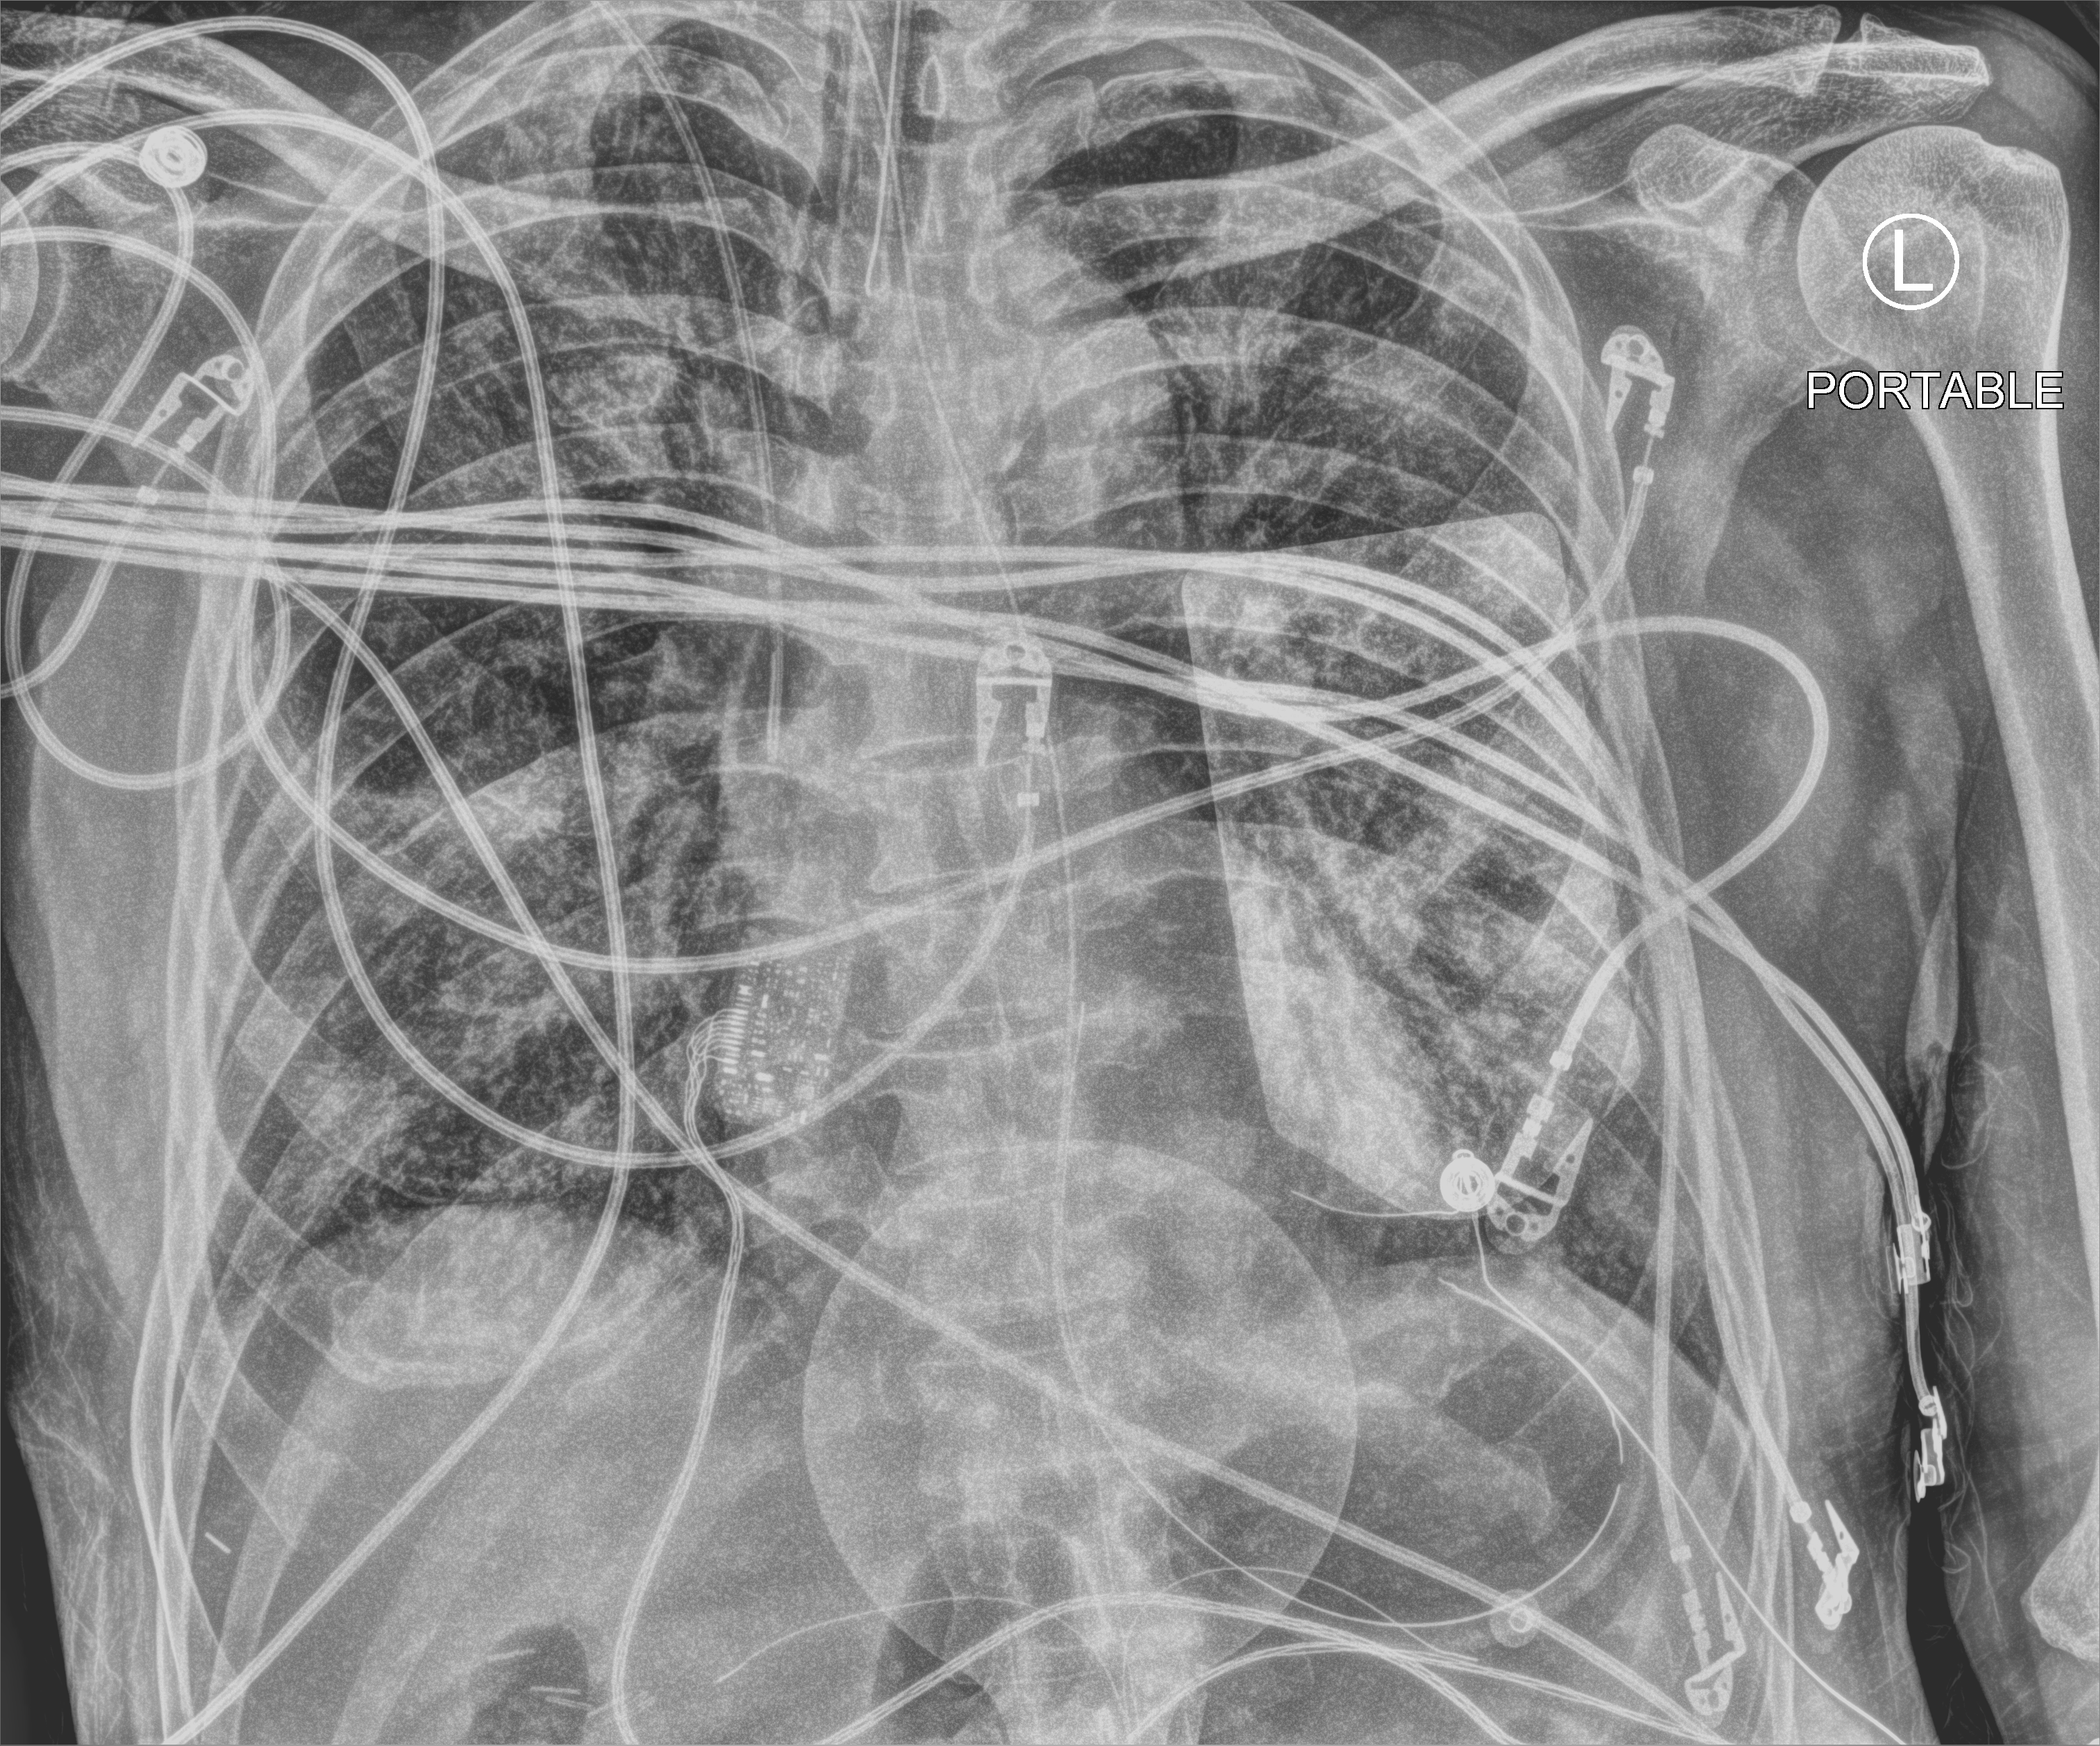
Portable chest radiograph, anteroposterior (AP) projection. Patient hospitalised with COVID-19; male, aged 60–74 years.
Hospital-stay facts (about this admission, not read from this image; timing relative to this image not recorded): mechanically ventilated during this hospital stay: yes; length of hospital stay: 31 days.